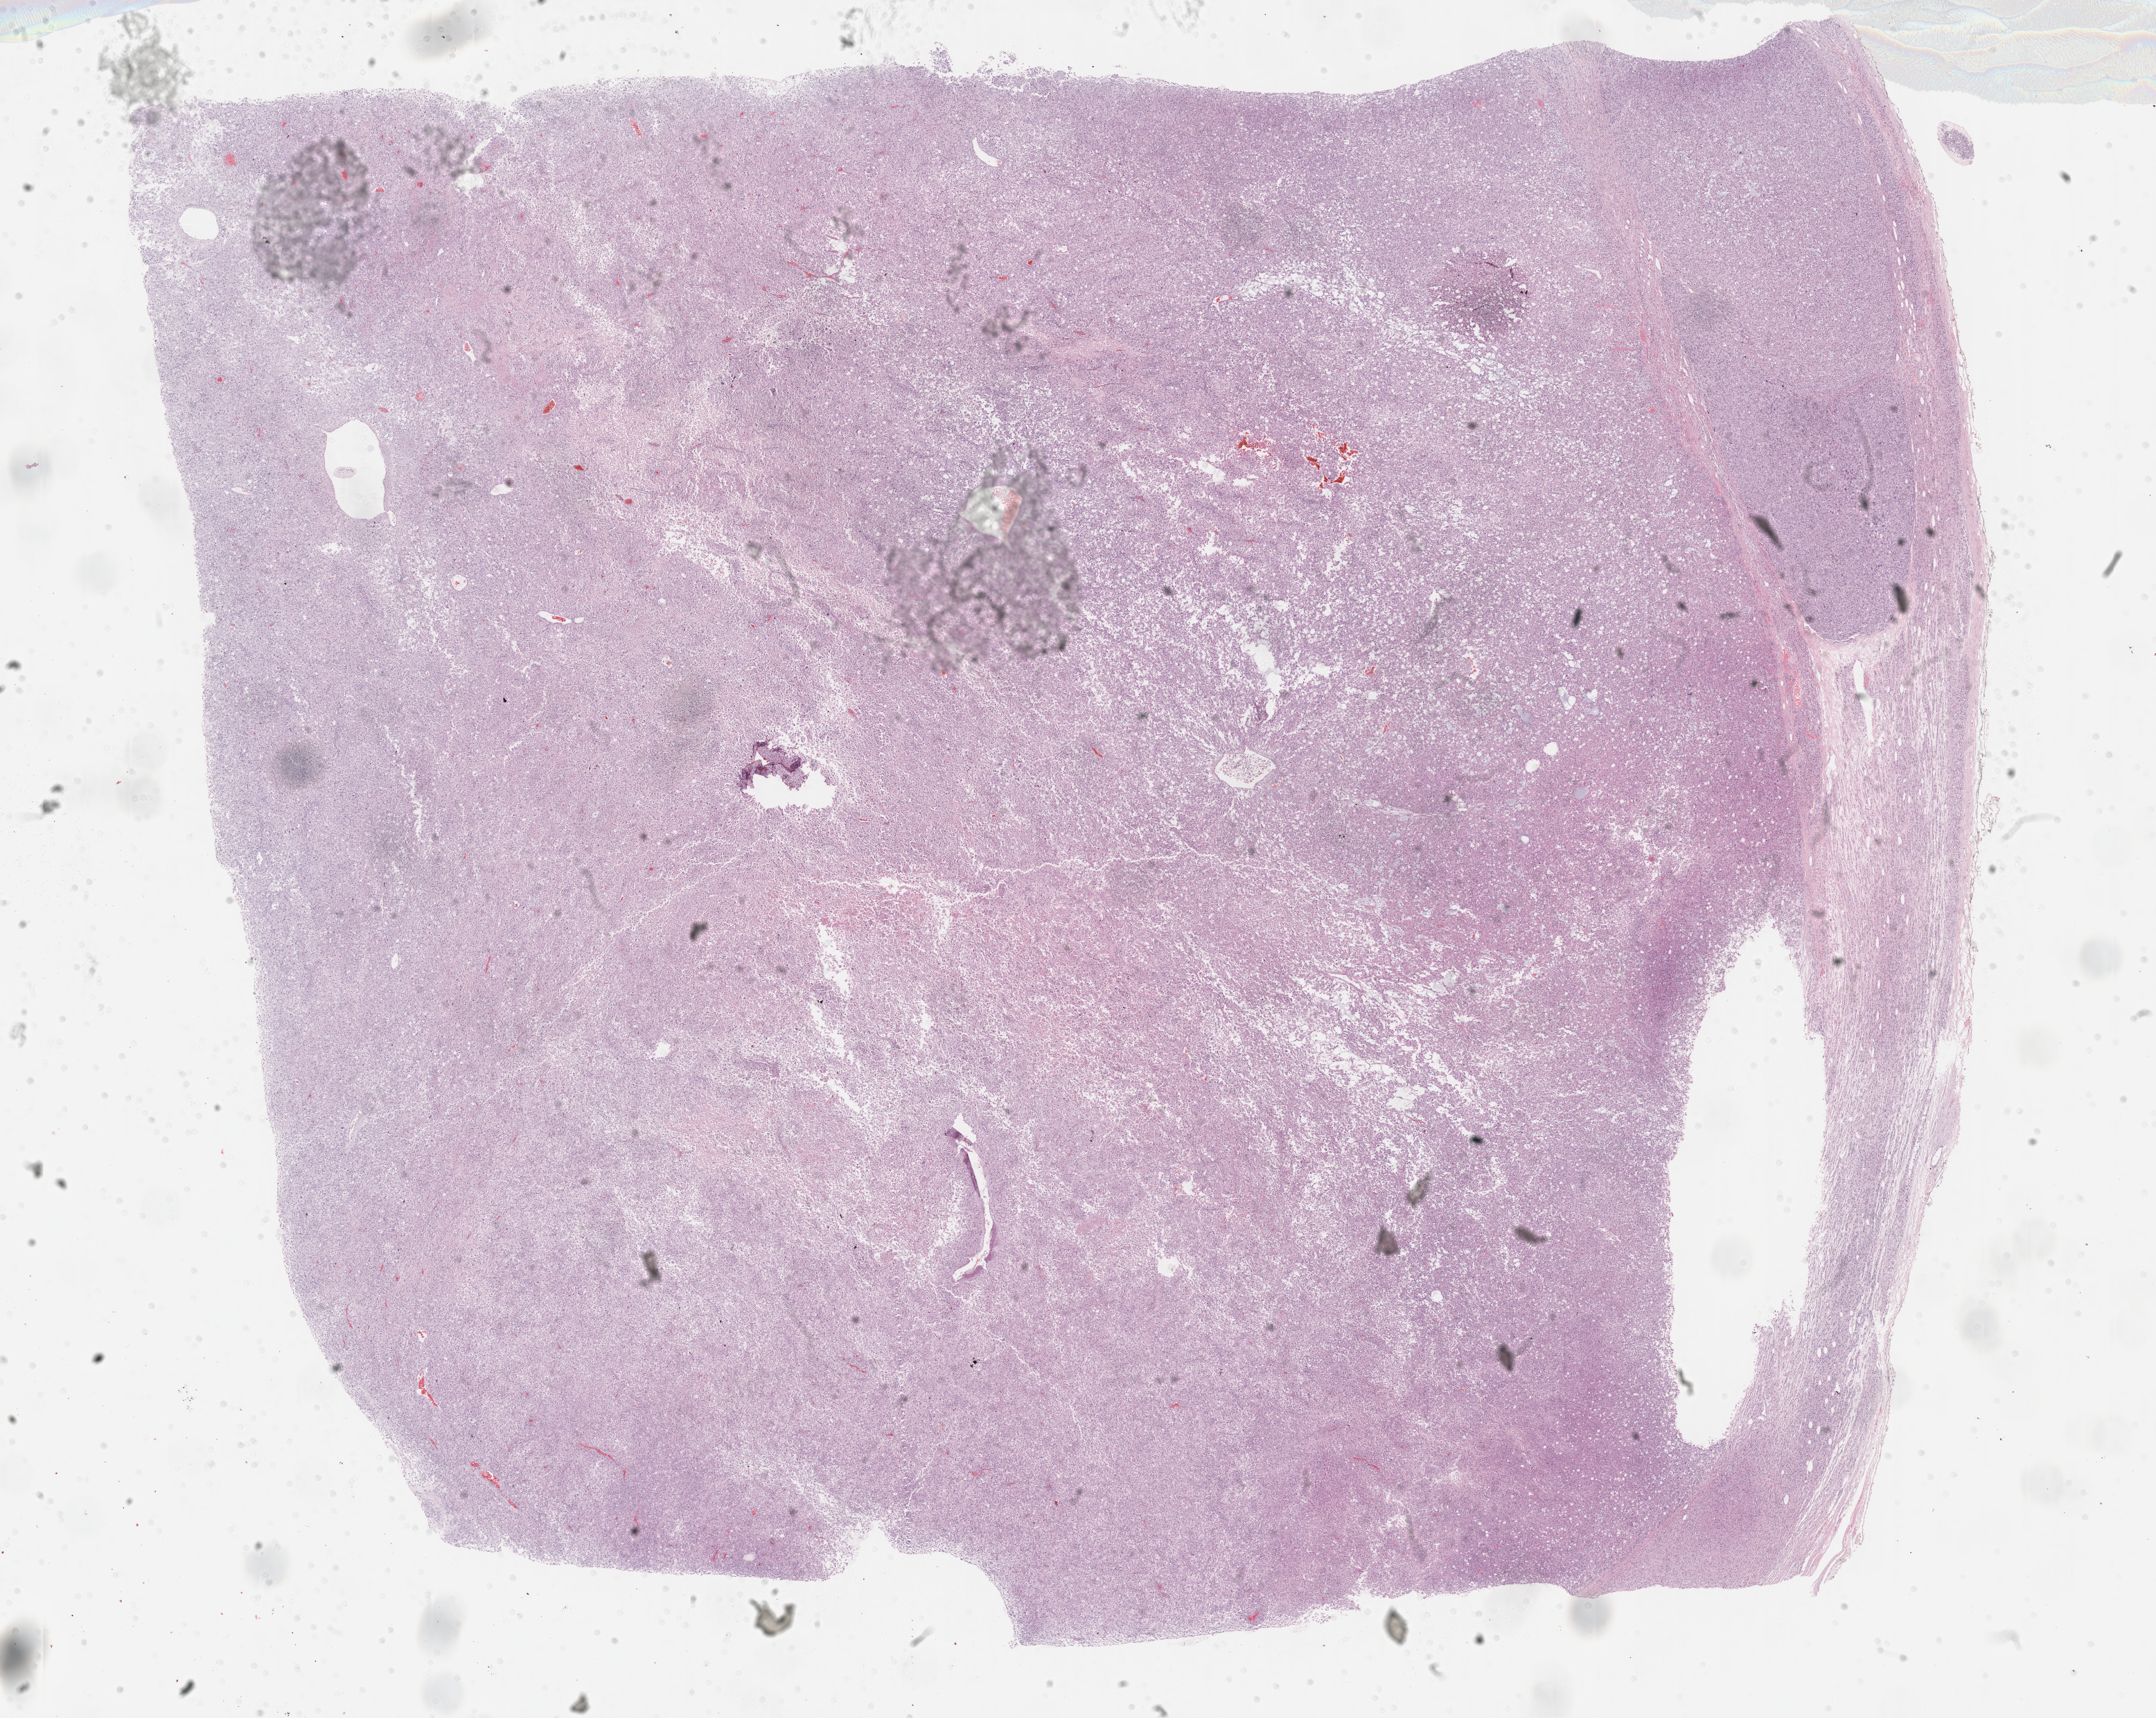
Digitized H&E tissue section (whole slide), shown as a low-resolution overview of the whole scanned area (about 25.2 x 20.1 mm). Formalin-fixed paraffin-embedded (FFPE) diagnostic section. Primary tumour sample from the adrenal cortex. Male, age 40 years at initial diagnosis.
Pathologic diagnosis: Adrenal cortical carcinoma (cortex of adrenal gland).